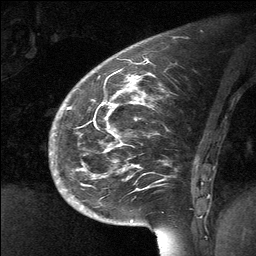
Breast MRI (dynamic contrast-enhanced), one sagittal slice. Slice 21 of 64 in the series (ordered by position). Dynamic contrast-enhanced study with each time point stored as its own series, time point 2 of 3 at this slice position (early post-contrast, ordered by acquisition time). 1.5 T. TE 4.8 ms, TR 27 ms. 256 × 256 image matrix. Patient: female, 39 years. Case-level facts recorded for this patient, not image findings: setting: breast cancer imaged before/during neoadjuvant chemotherapy; receptor status: HER2-positive.
Structures marked on this image (semi-automatic segmentation, software-assisted and operator-edited):
- analysis volume of interest (the breast-tissue region the enhancement analysis was run in; not a lesion): box from (x=70, y=69) to (x=202, y=224) px
- tumour enhancement mask (voxels above the 90 % enhancement threshold inside the analysis volume of interest): (x=104, y=76)–(x=138, y=167)